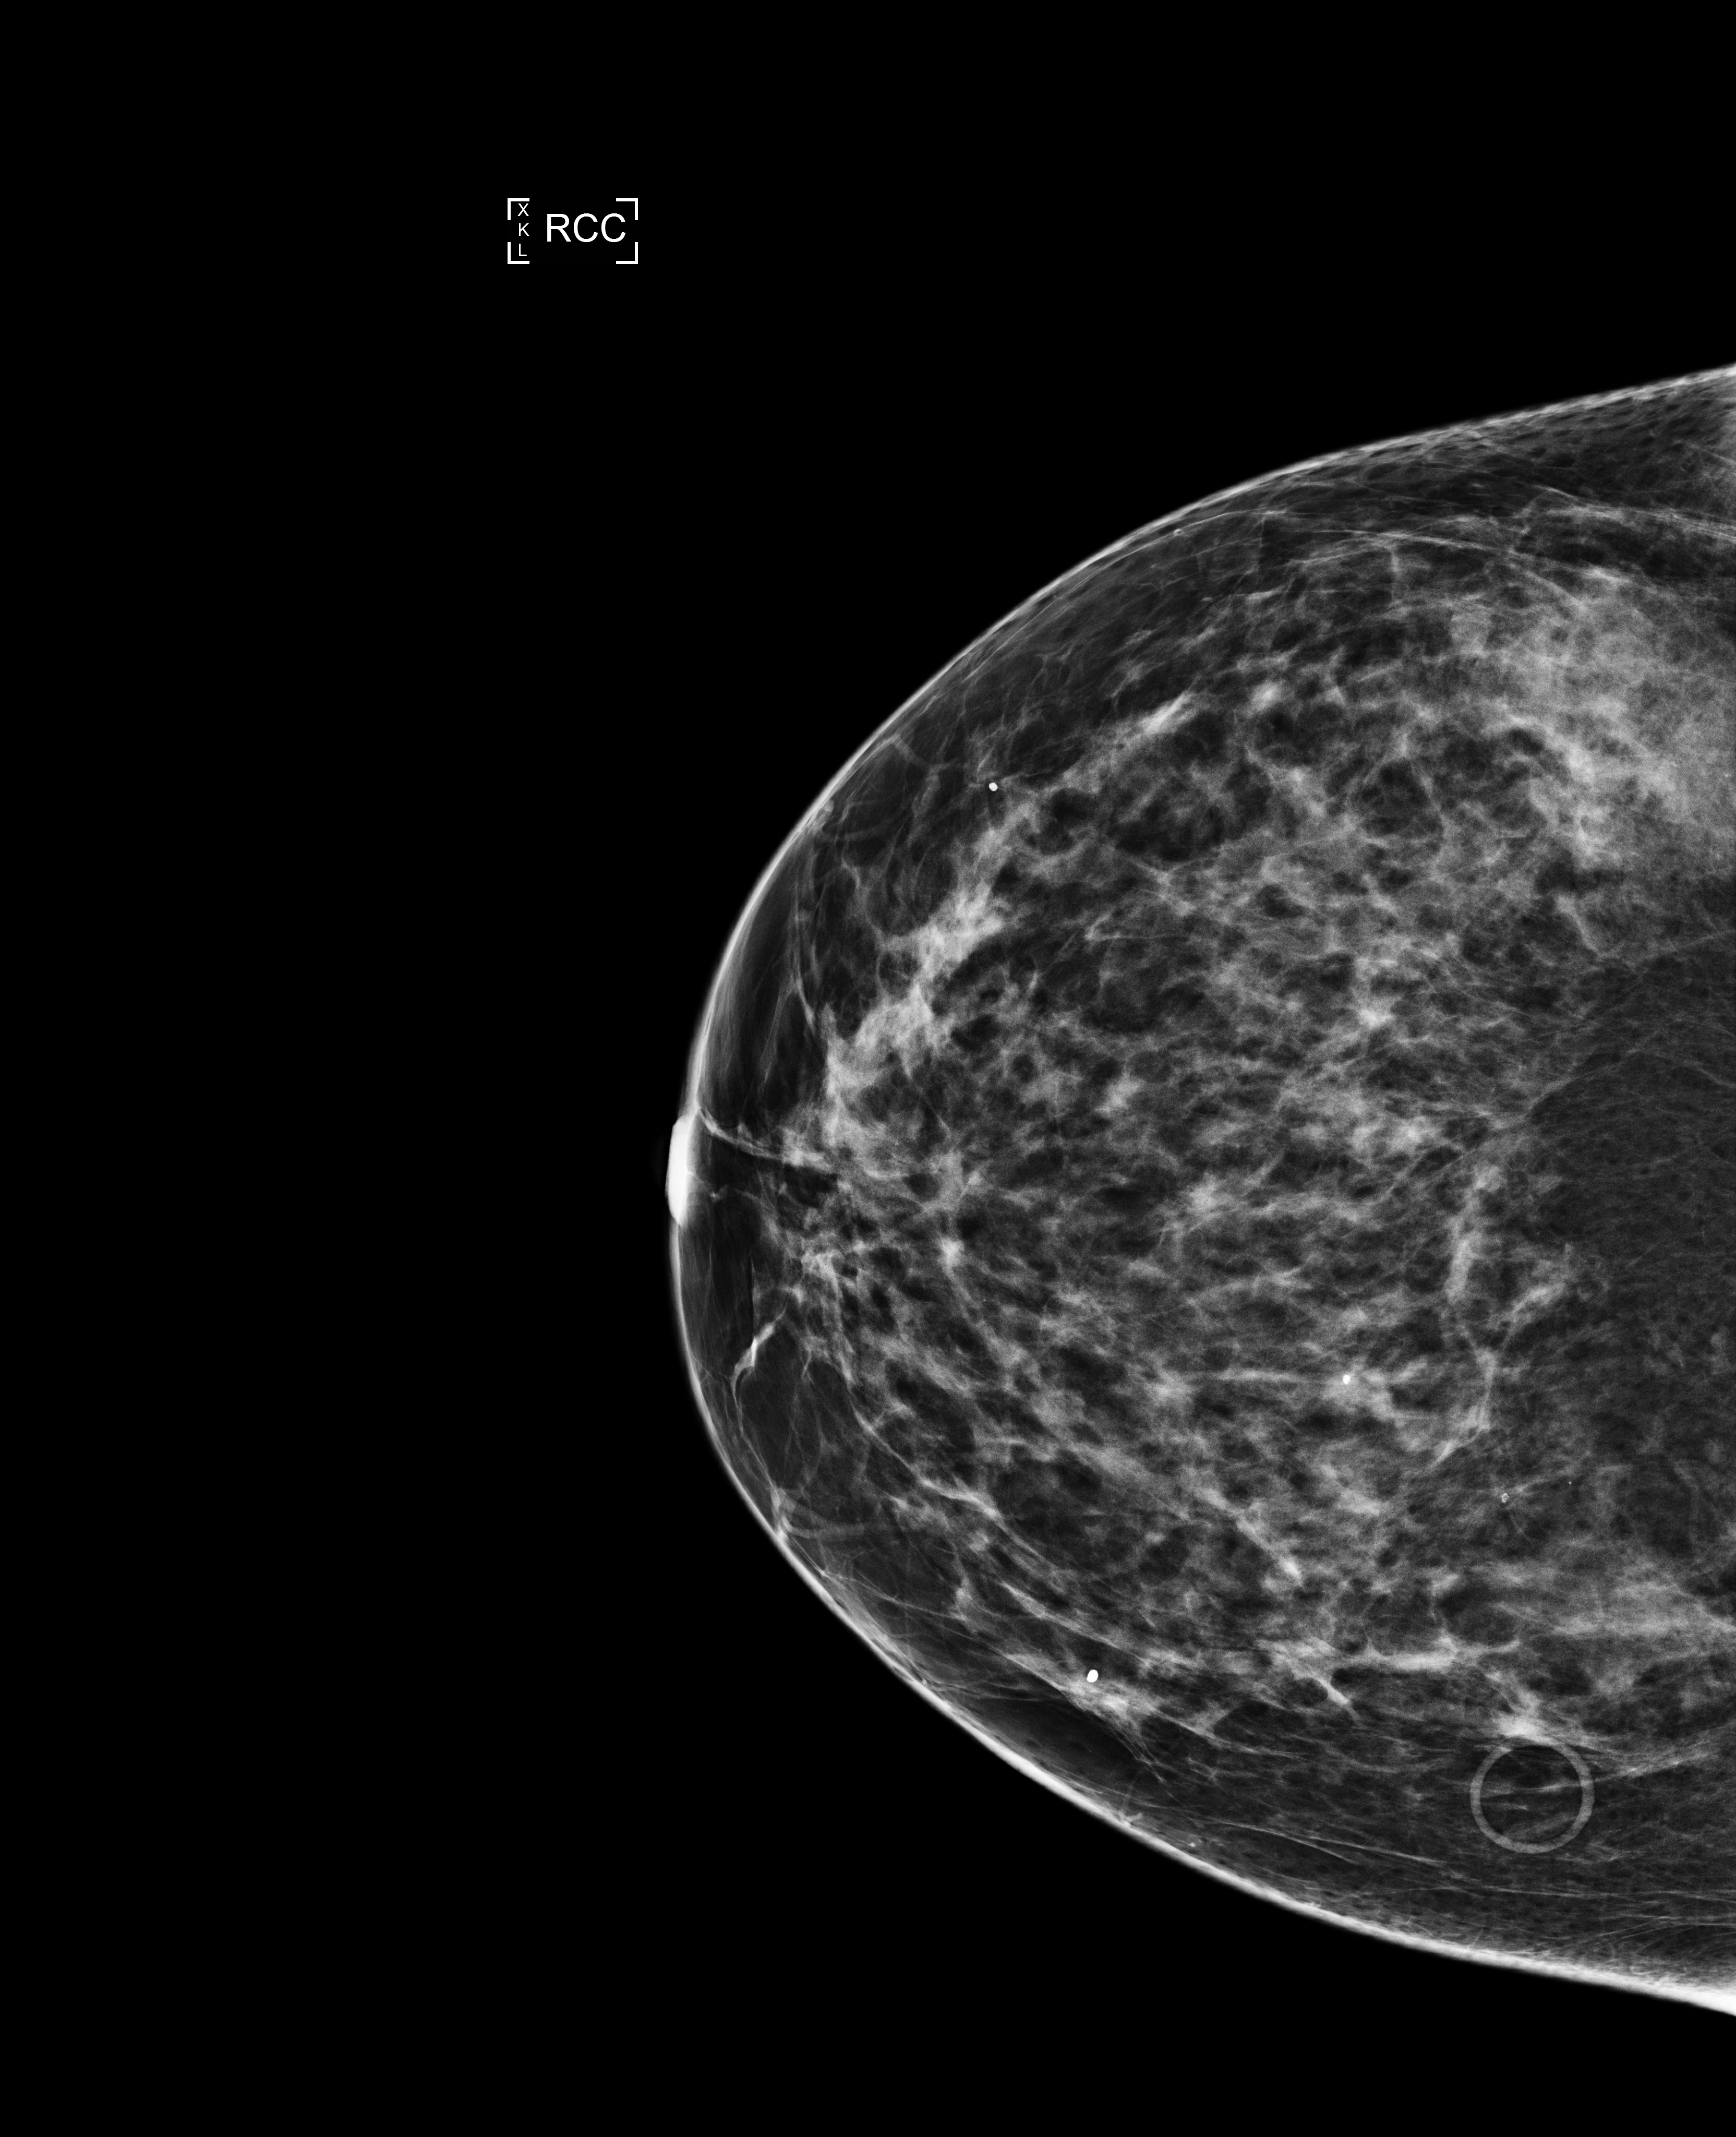
Annual screening mammography examination. Patient: female, 46 years.
Image type: full-field digital mammogram. Breast: right. Projection: CC view.